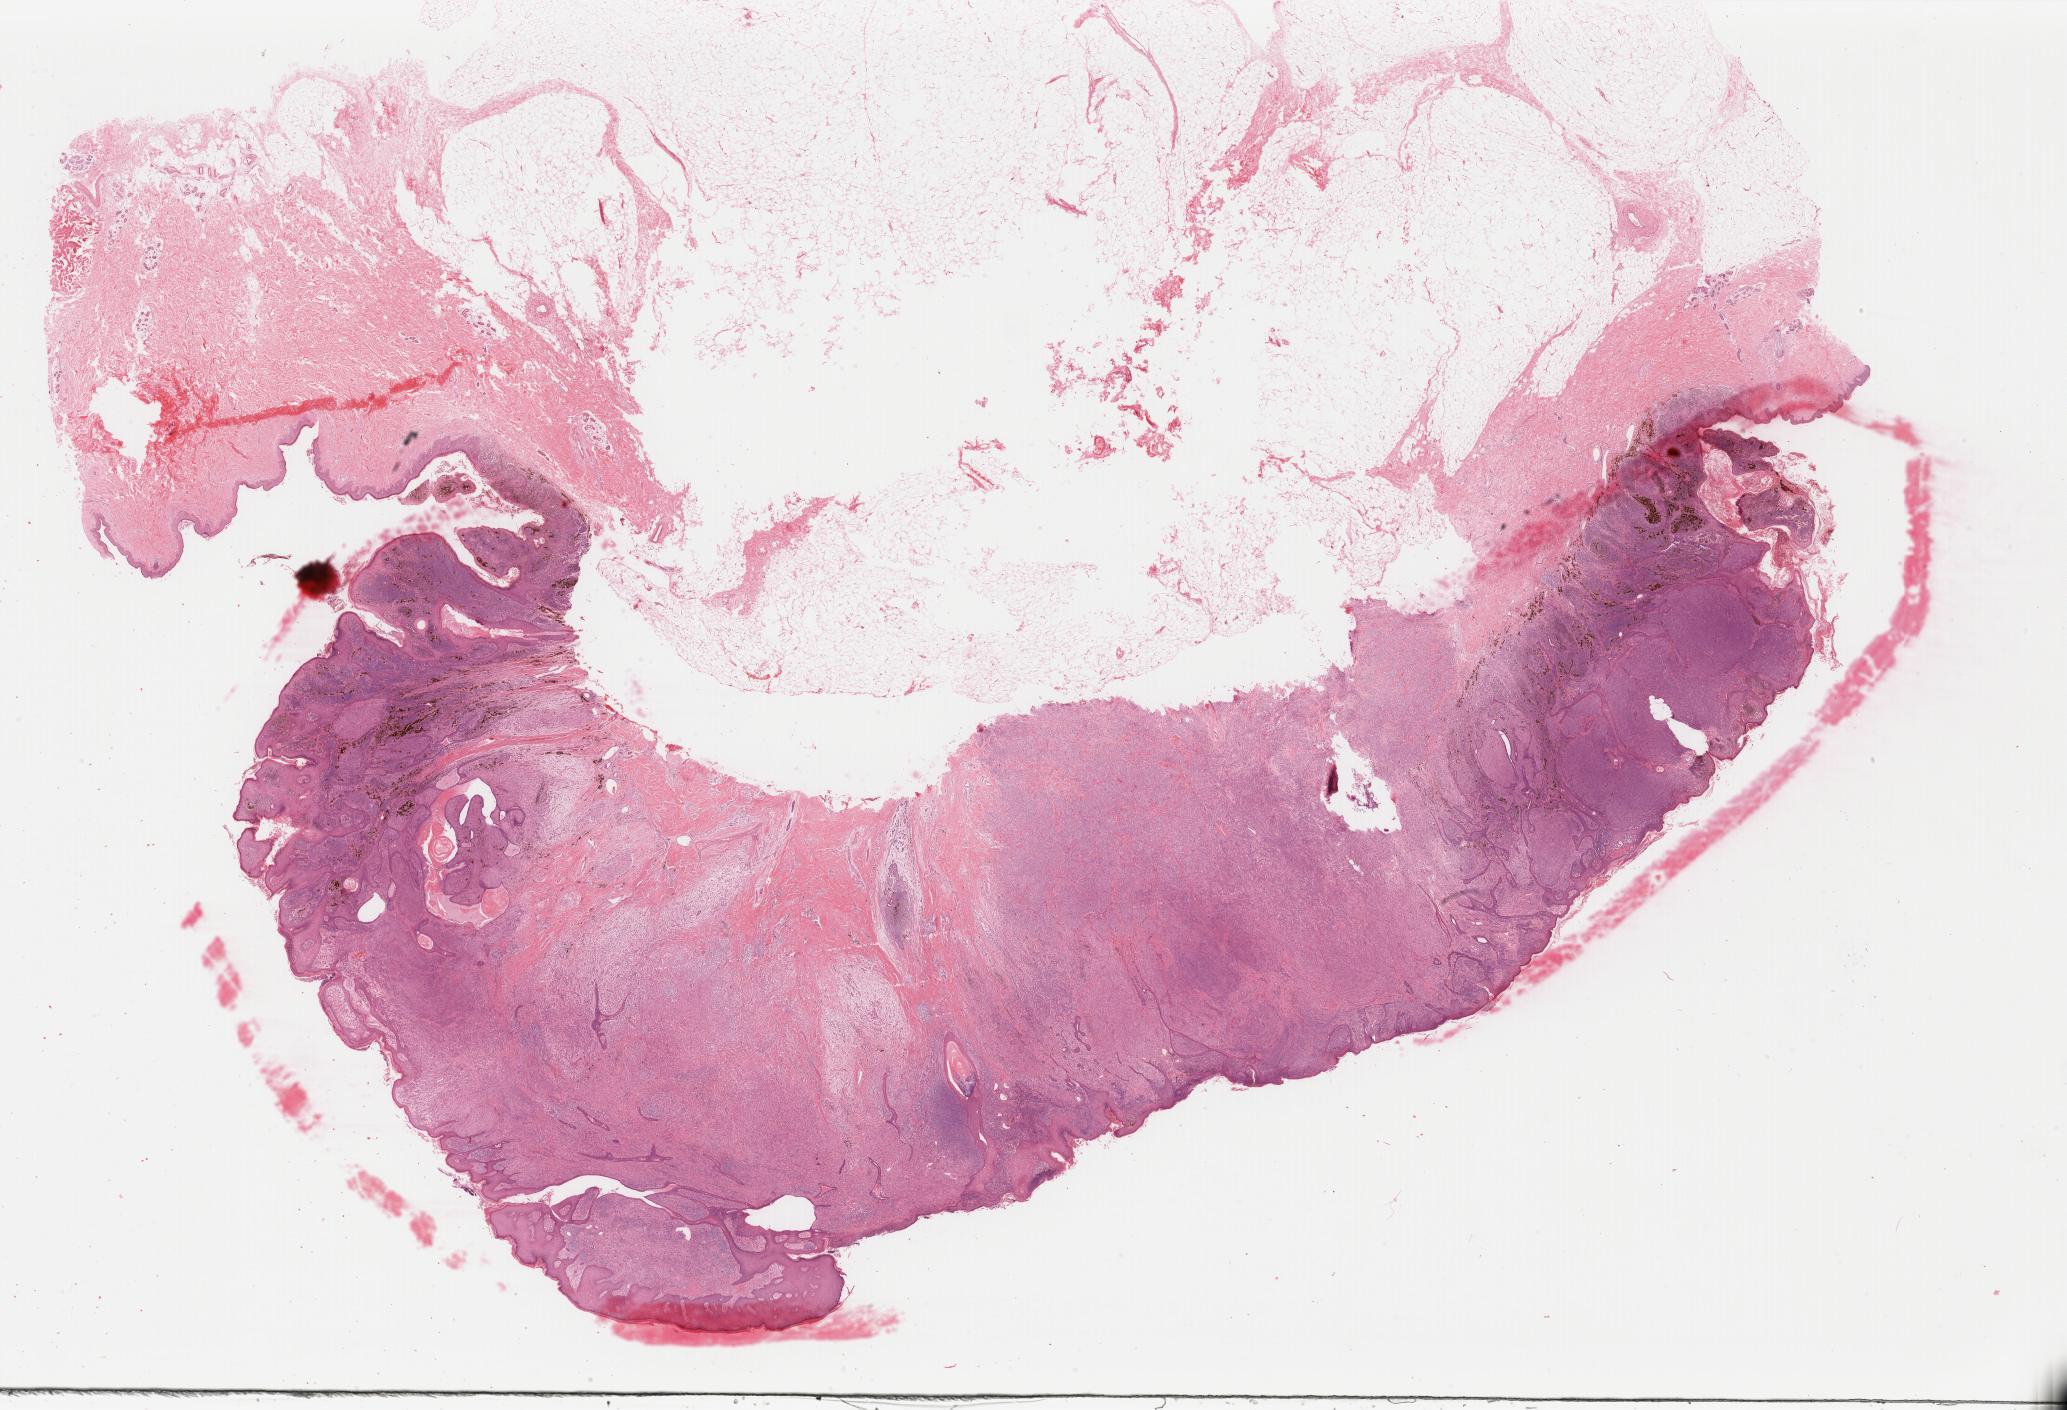
Whole-slide histology image, H&E, low-resolution overview of the scanned area, about 32.8 x 22.4 mm (from a 40x scan); formalin-fixed paraffin-embedded (FFPE) diagnostic section; primary tumour sample from the skin. Patient: female, age at initial diagnosis 75 years.
AJCC pathologic stage: IIC. Diagnosis: Malignant melanoma, NOS.